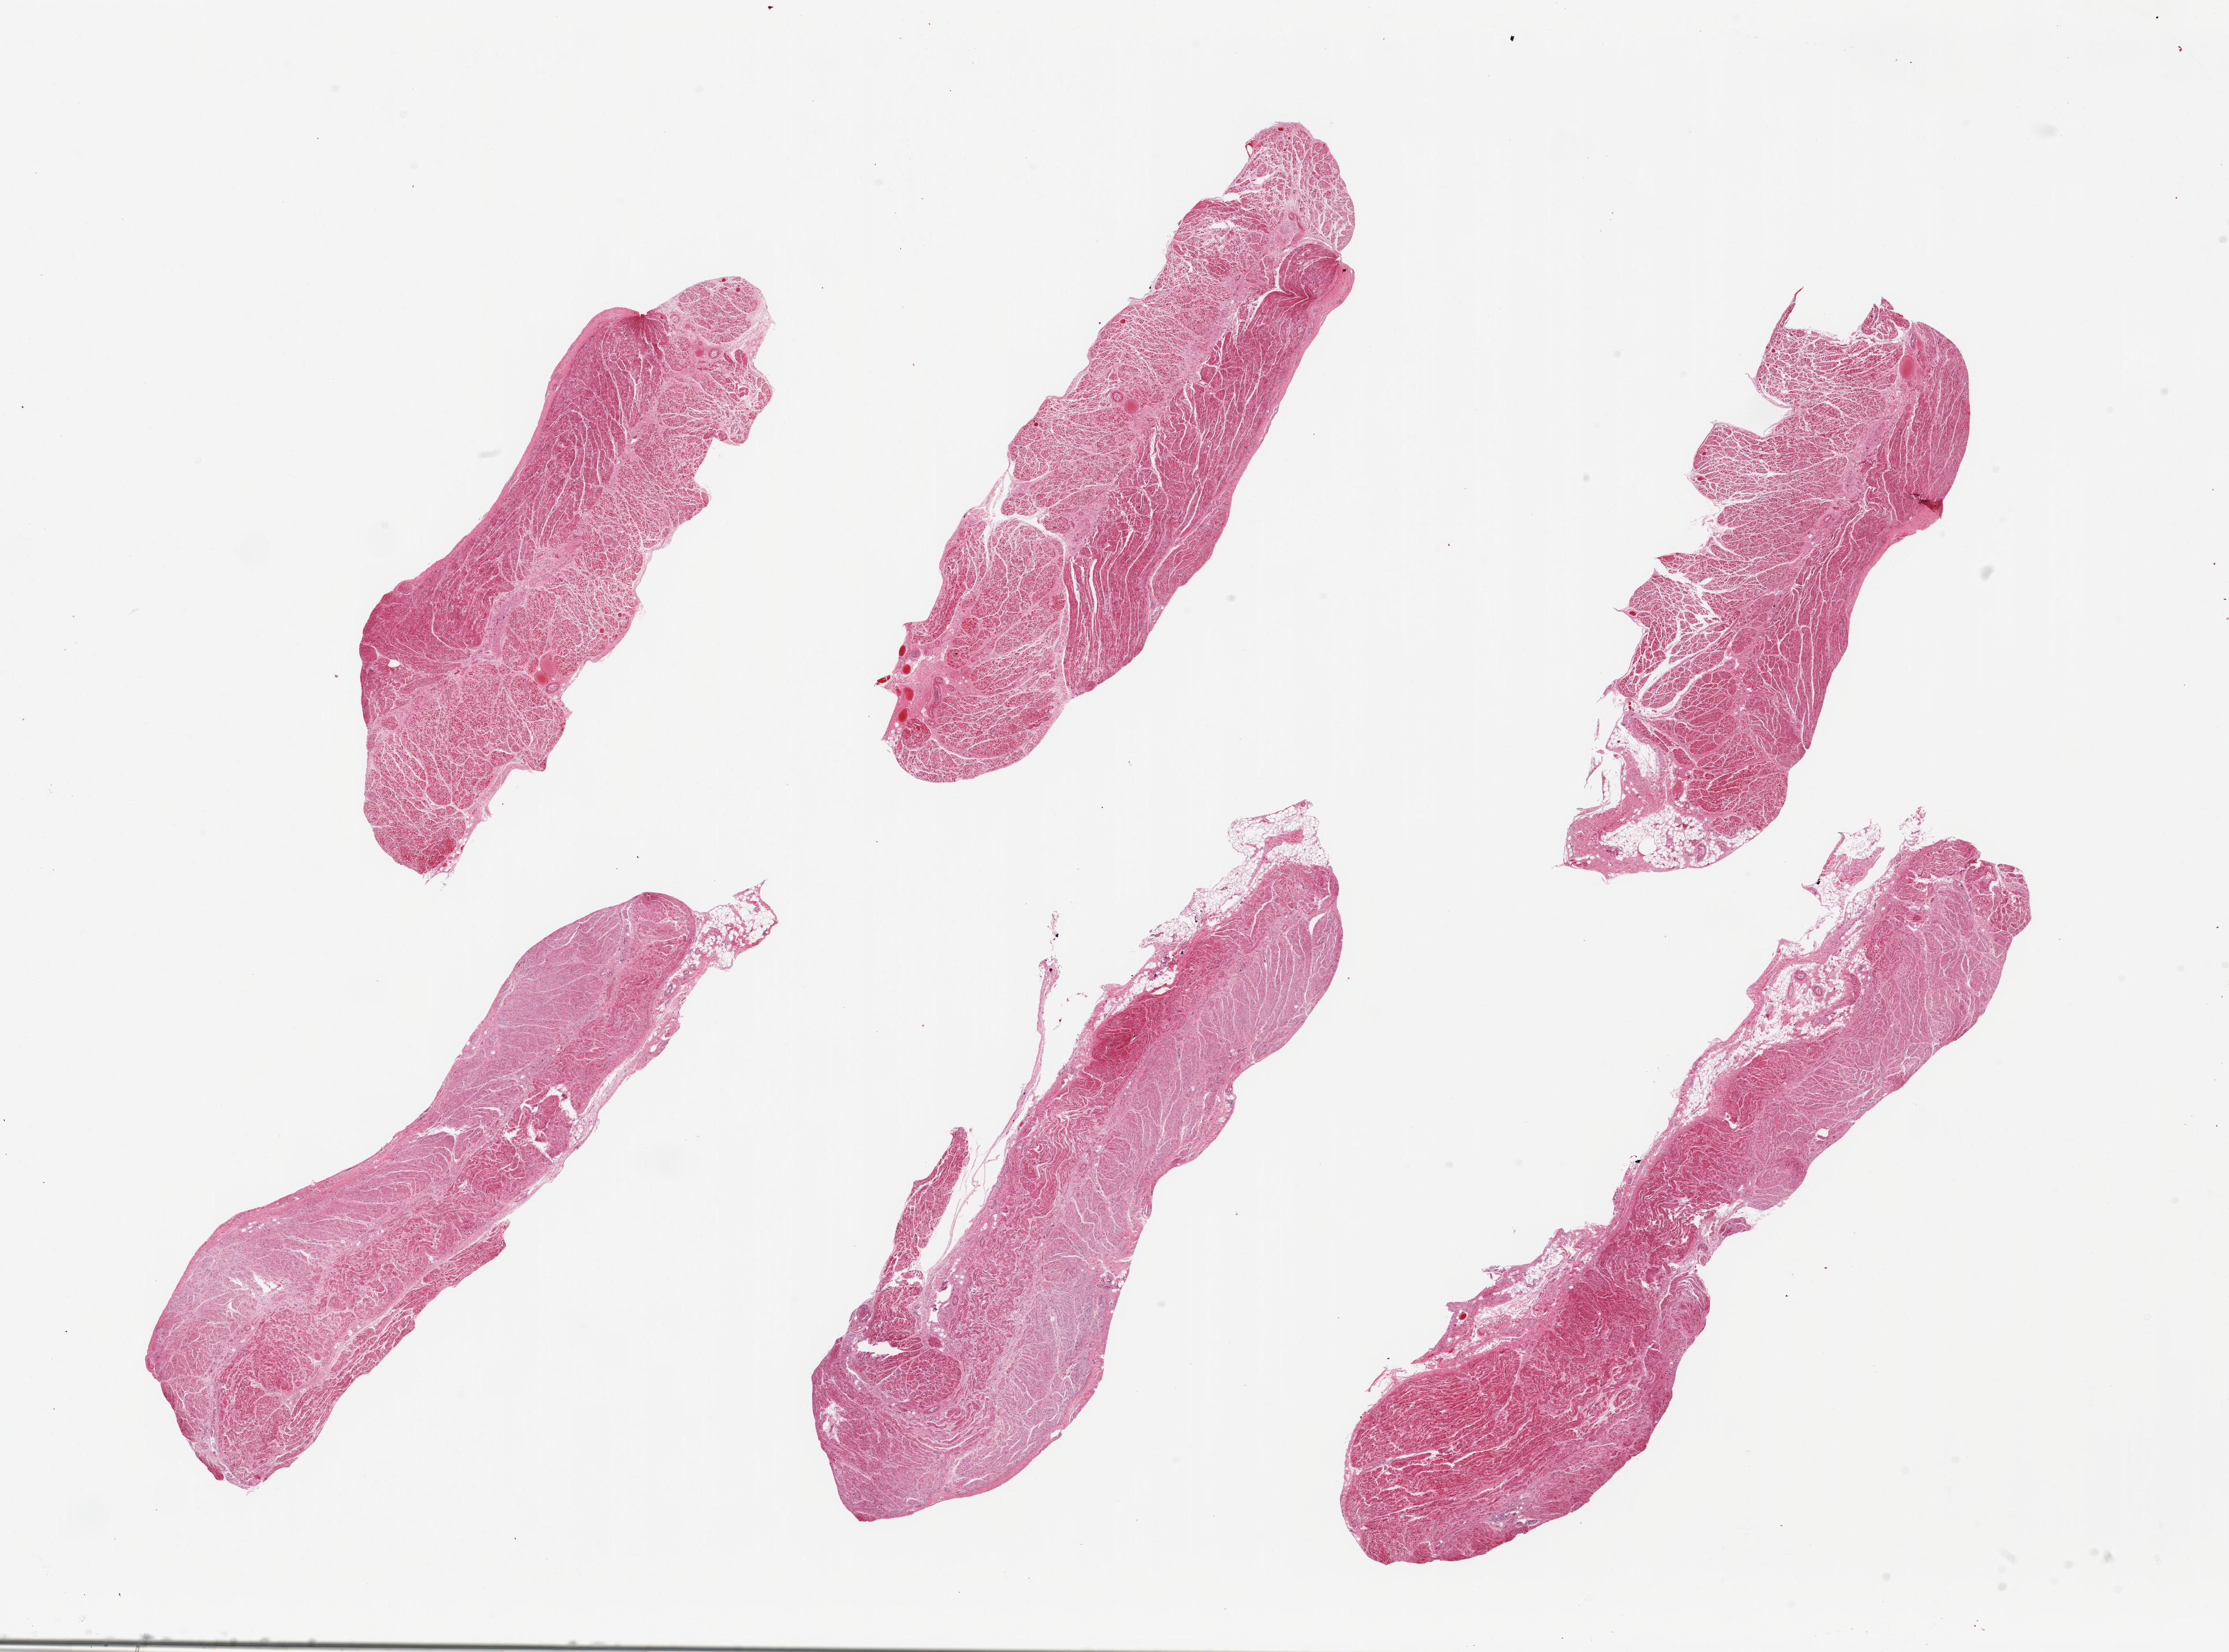
Whole-slide image, H&E stain — low-resolution overview of the scanned area, about 30.5 x 22.6 mm, PAXgene-fixed paraffin-embedded (PFPE) section, sampled site (target tissue): gastroesophageal junction, tissue donor sample. Donor: male.
Reviewer comment on this tissue sample: 6 pieces; target muscularis, few with small attachment of fat.